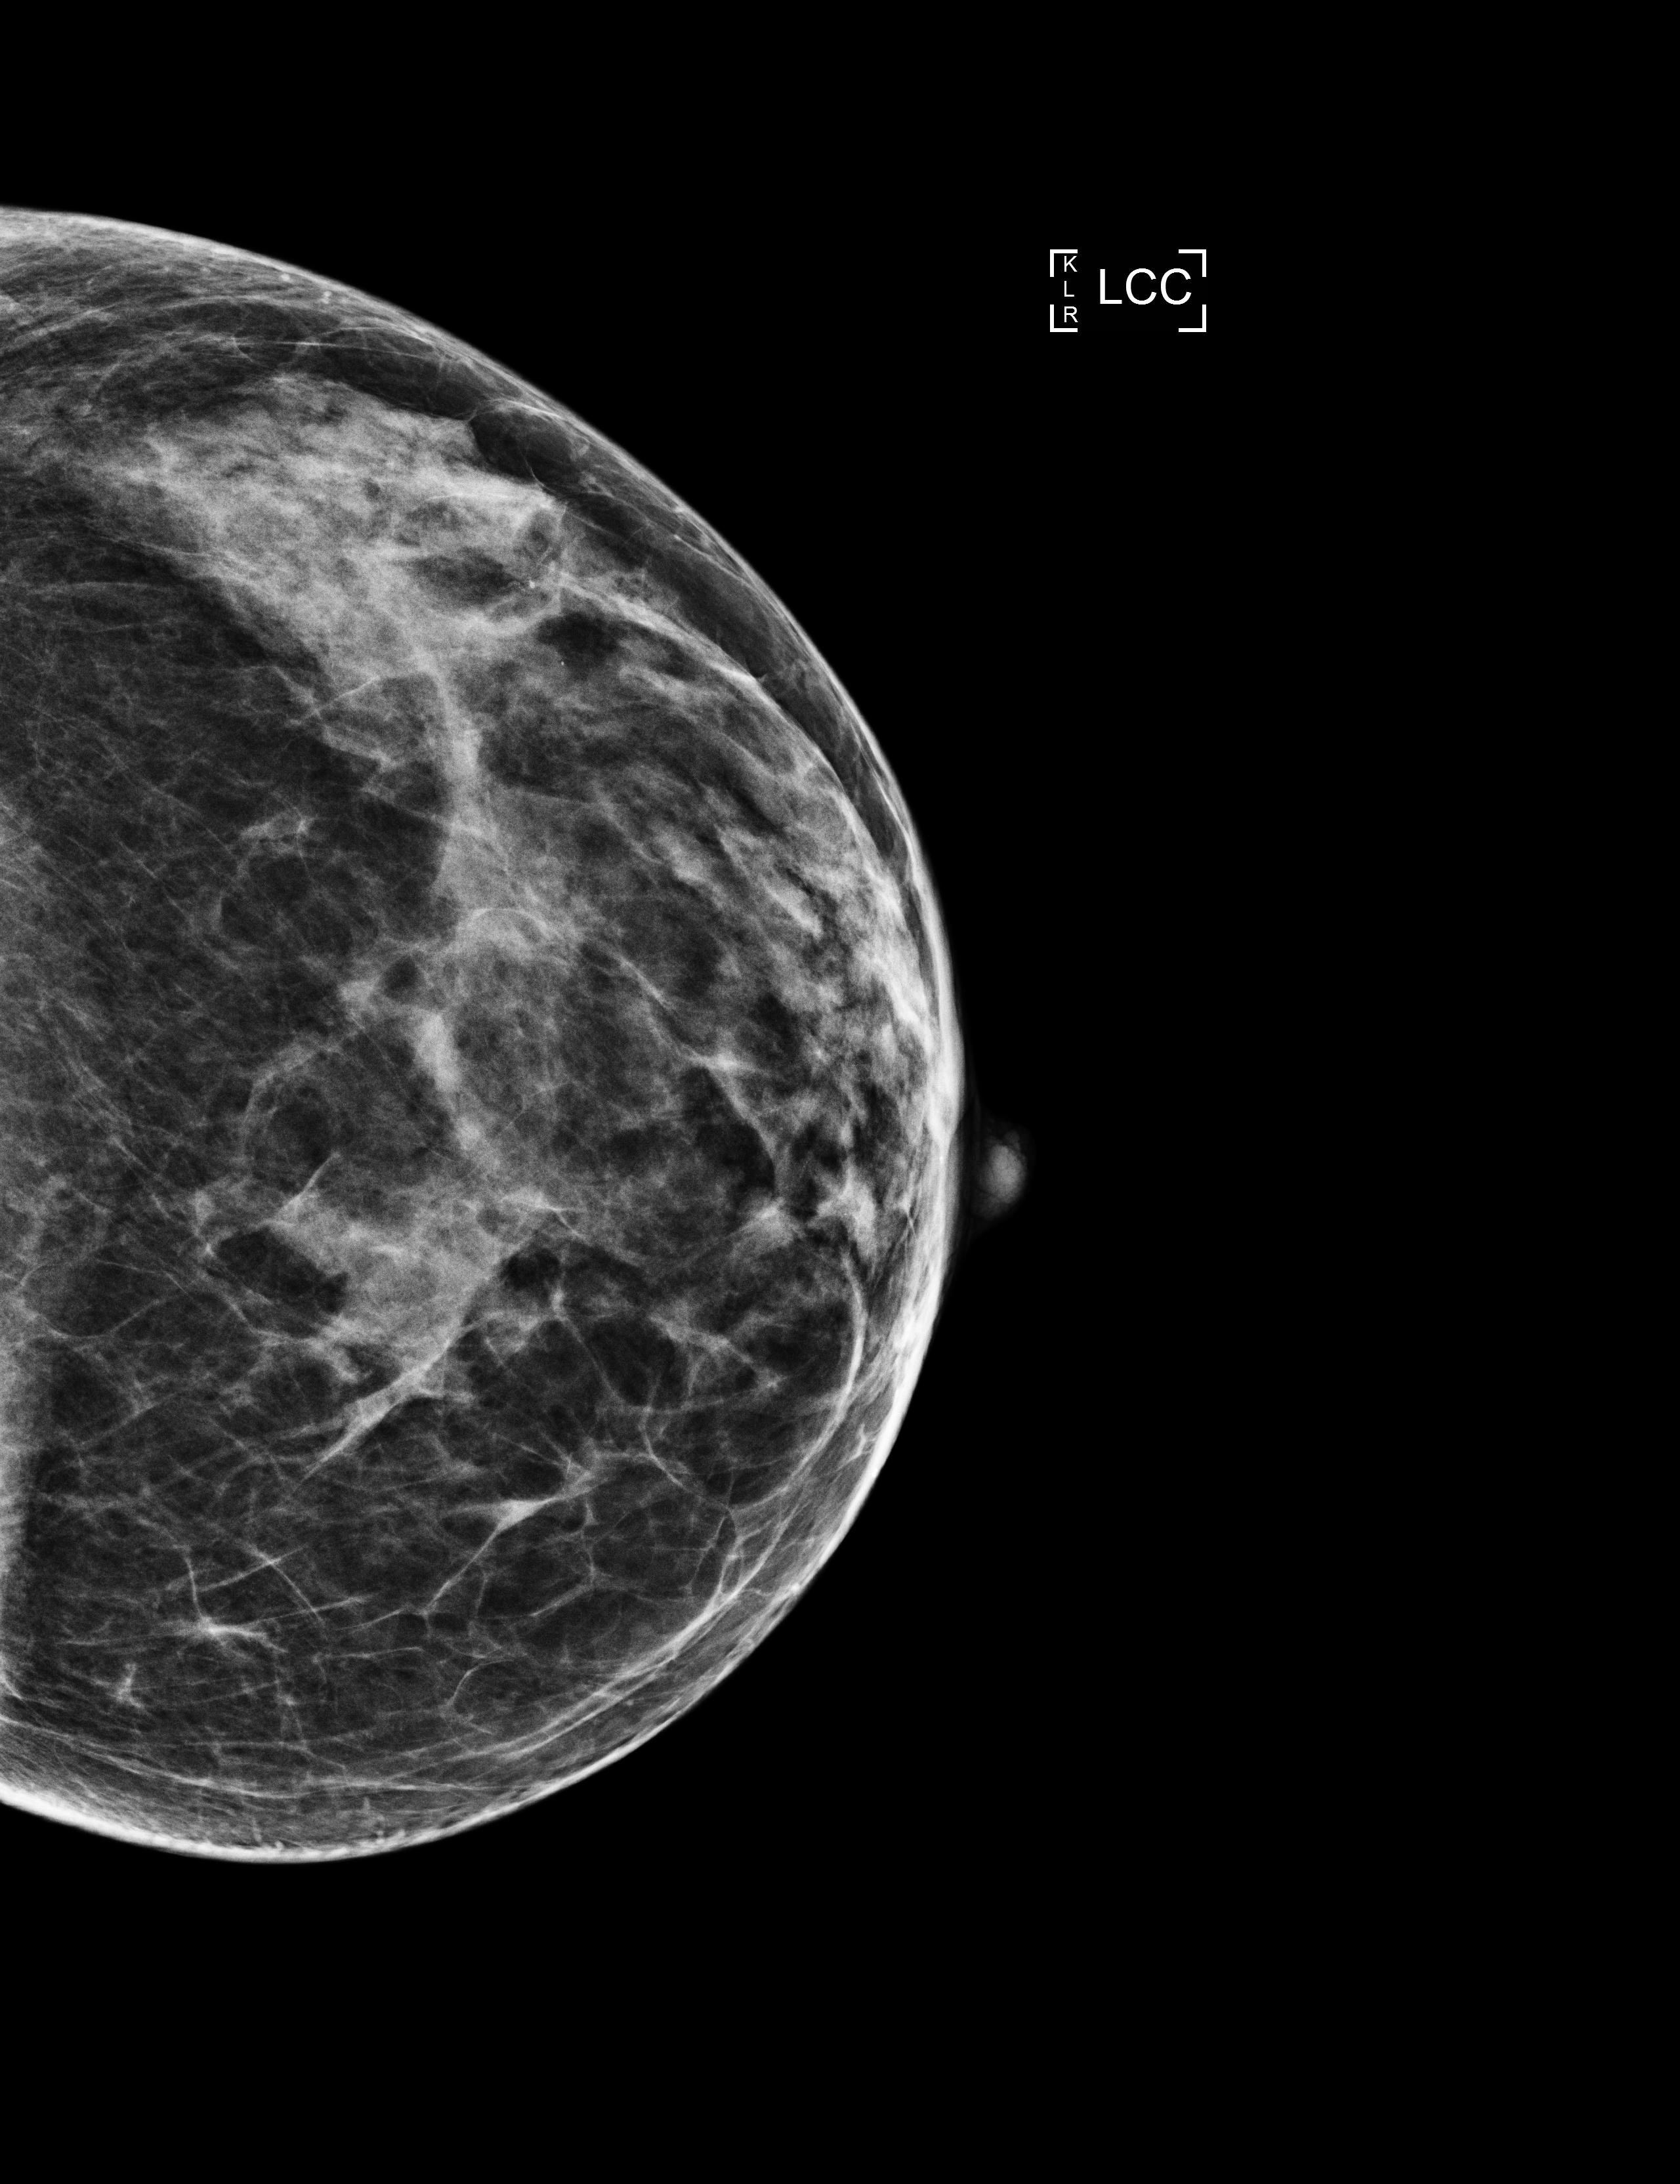
Digital mammogram (FFDM), left breast, CC view, annual screening mammography examination, compressed breast thickness 43 mm. Female patient, age 62 years.
- BI-RADS breast density category at the screening exam (both breasts, scale 1–4): 3
- final BI-RADS category for the screening round (tomosynthesis exam, both breasts): category 2
- recall: no recall after this screen